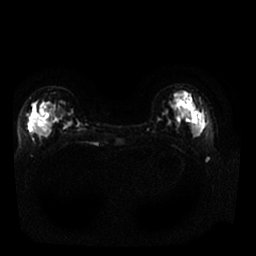
Breast MRI, one axial slice; position 7 of 25 along the scan axis; diffusion-weighted series; image 2 of 4 stored at this slice position (different b-values; order by instance number); 1.5 T; 4 mm slice thickness; 256 × 256 image matrix, field of view 340 × 340 mm. Female patient.
Annotated regions visible in this slice (expert manual segmentation):
- tumour on diffusion-weighted imaging: bounding box (x1, y1, x2, y2) in pixels: (31, 105, 42, 135)